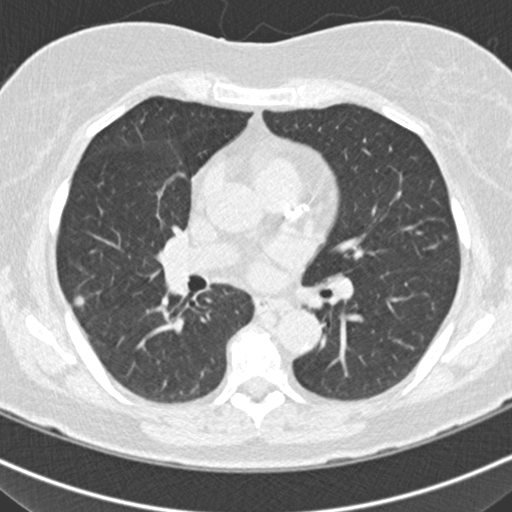
Low-dose screening chest CT, one axial slice. Slice 102 of 160 in the series (ordered by position). Reconstruction kernel B30f. Lung window (W 1500 / L -600 HU). 2 mm slice thickness. 512 × 512 image matrix, field of view 316 × 316 mm.
Annotated regions visible in this slice (manually delineated by an expert):
- lesion 2 (tumor, middle lobe of right lung): bounding box <74,295,85,307> (left, top, right, bottom; pixels)